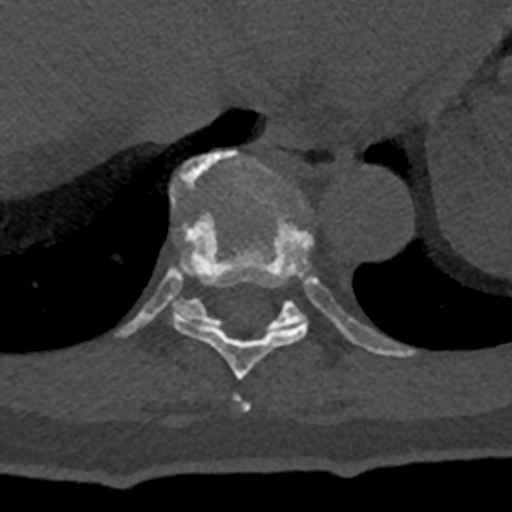
CT including the spine, one axial slice; position 637 of 797 along the scan axis; reconstruction kernel Br40s/3; bone window (W 1800 / L 400 HU); 512 × 512 image matrix. Patient: male, 74 years. Case-level facts recorded for this patient, not image findings: primary cancer: renal.
Structures marked on this image (semi-automatically segmented with operator editing):
- T10 vertebra: bounding box <115,150,415,357> (left, top, right, bottom; pixels)
- T8 vertebra: <235,395,251,411>
- T9 vertebra: <171,218,312,380>